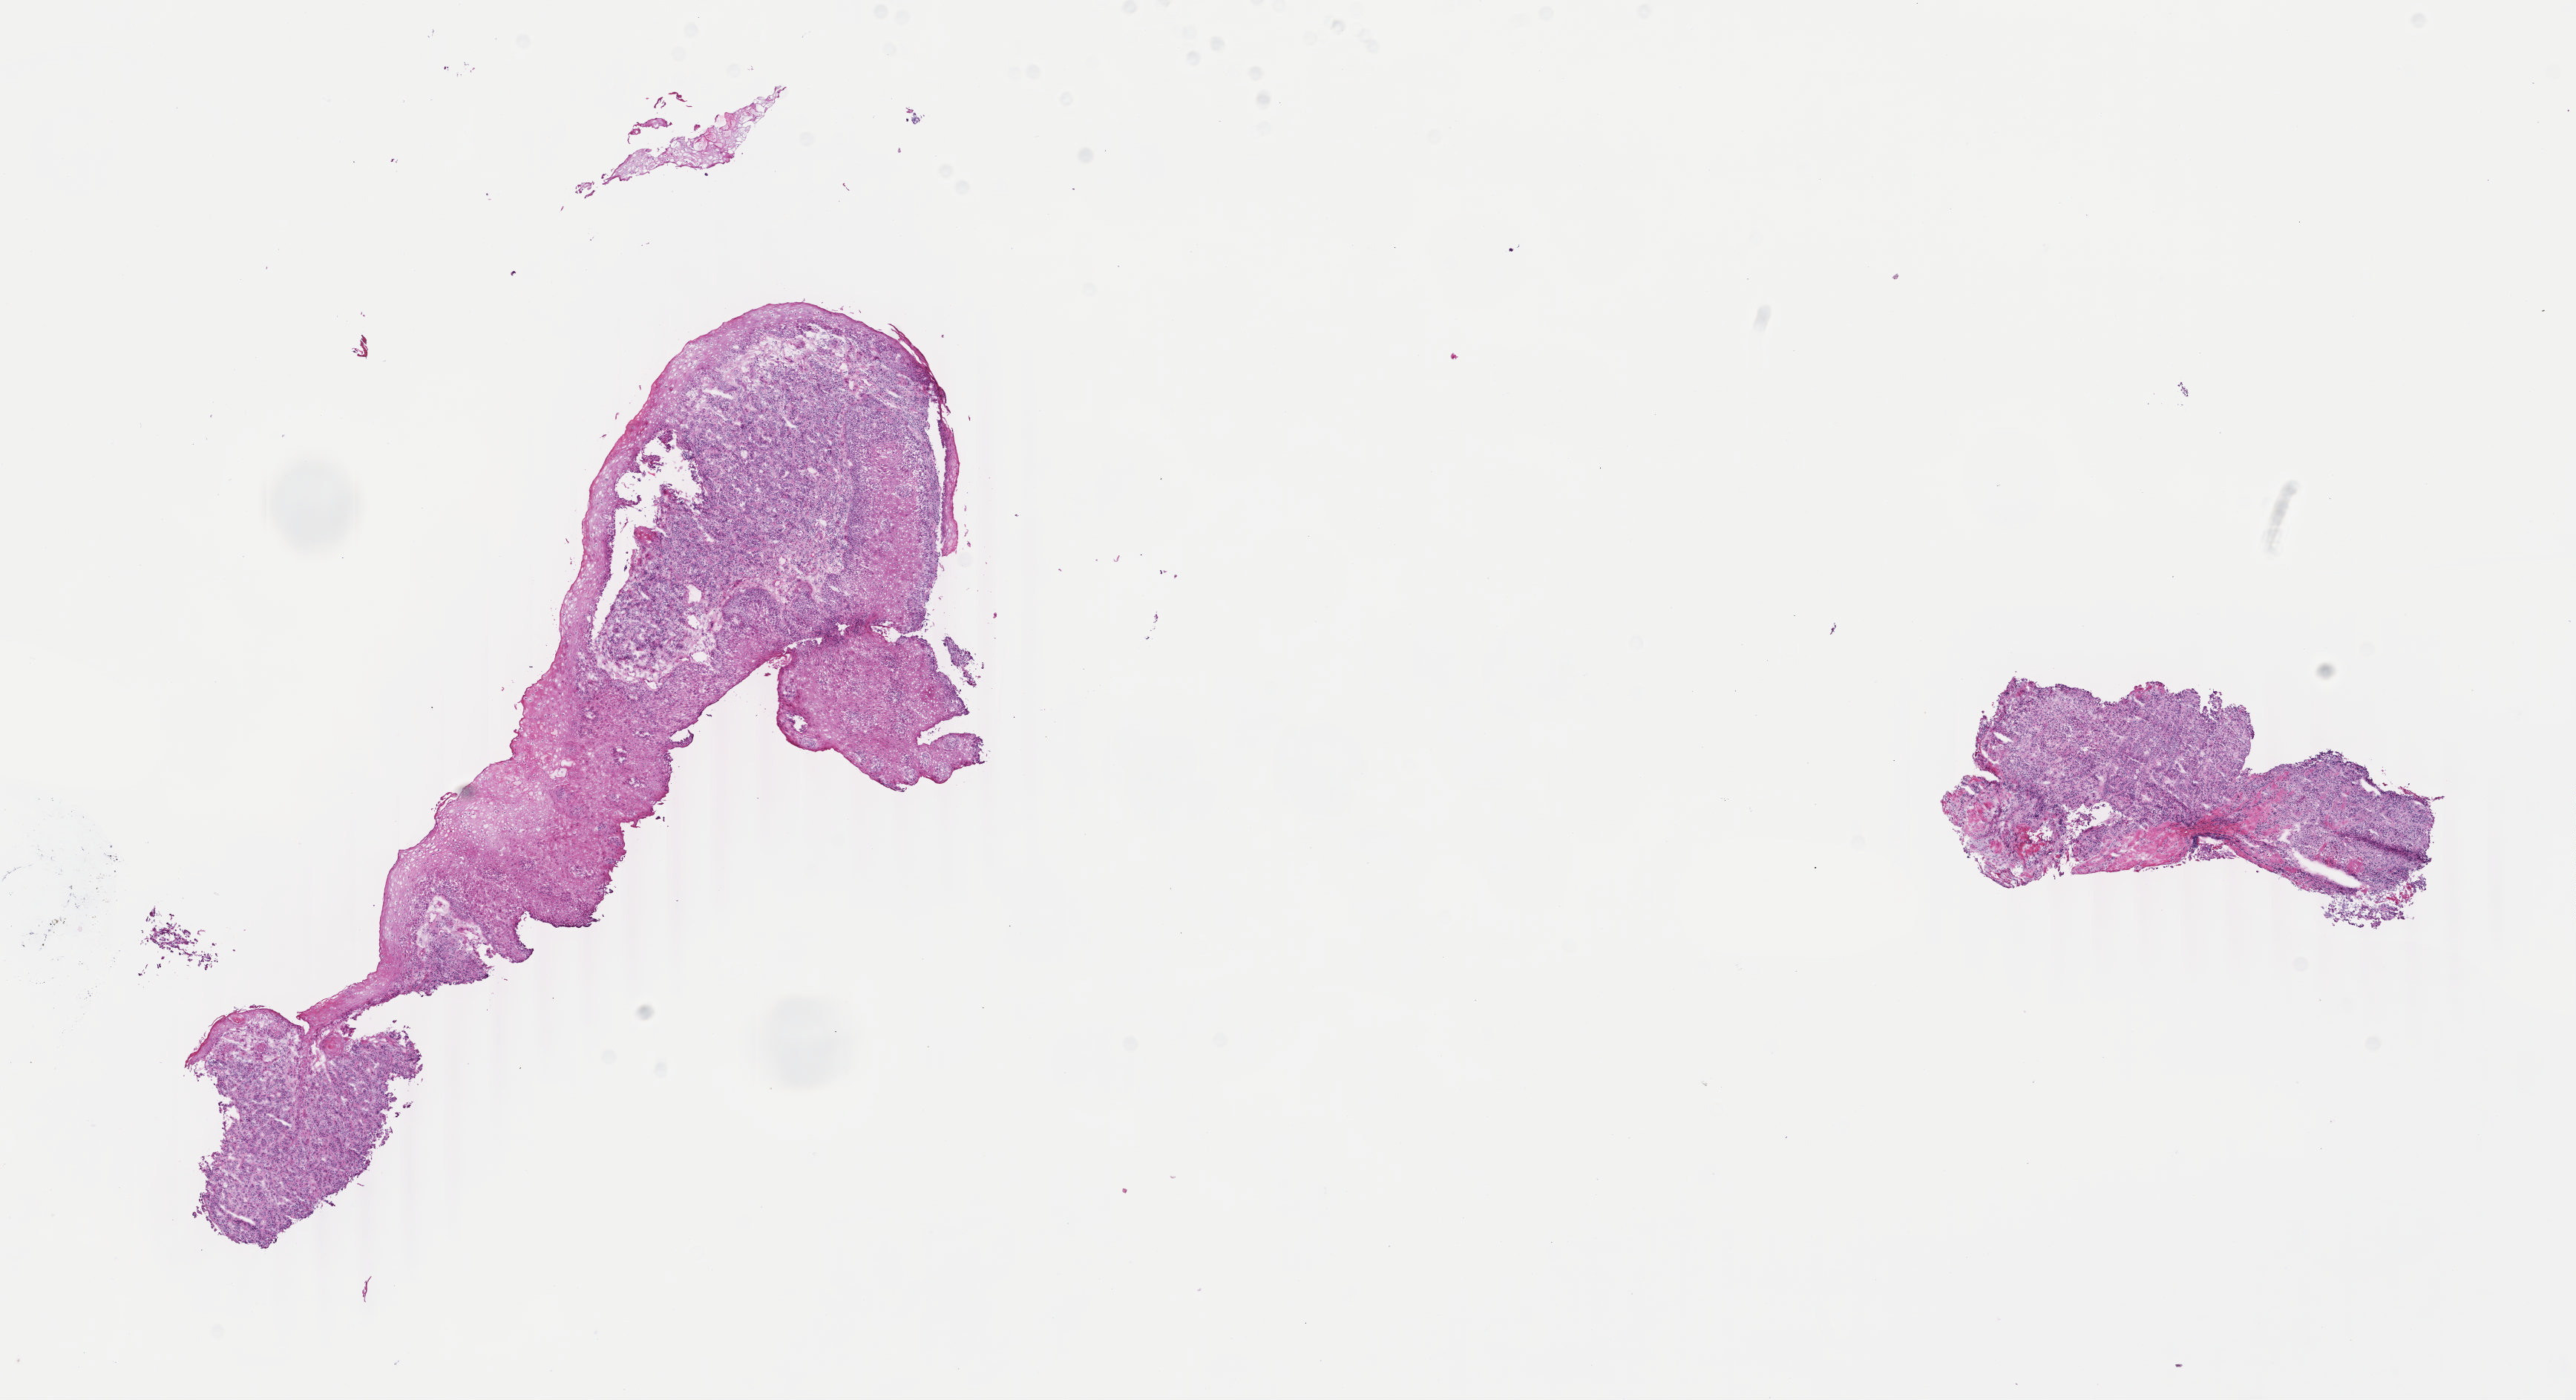
H&E whole-slide image, whole scanned area (about 13.8 x 7.5 mm, slide scanned at 40x) shown as a low-resolution overview; frozen section from the top of the tissue portion; esophagus, primary tumour sample. Male patient; age at initial diagnosis 59 years. Slide review estimates, as recorded: tumour cells 40%, tumour nuclei 60%.
Histologic diagnosis: Adenocarcinoma, NOS (lower third of esophagus).